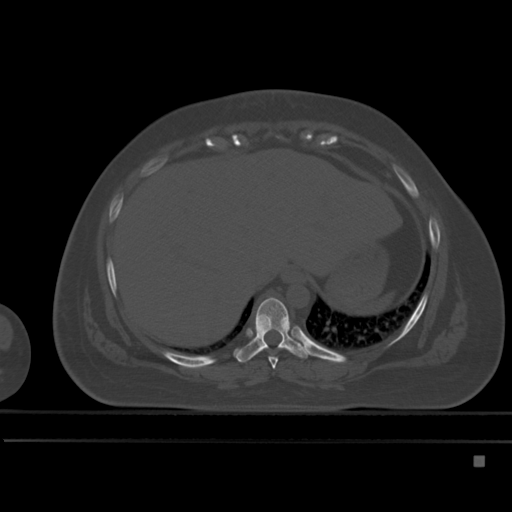
CT including the spine, one axial slice. Position 266 of 495 along the scan axis. Bone window (W 1800 / L 400 HU). 1.5 mm slice thickness. 512 × 512 image matrix, field of view 404 × 404 mm. Female patient, age 33 years. Case-level facts recorded for this patient, not image findings: primary cancer: breast; vertebrae with lytic lesions (as recorded): T1.
Annotated regions visible in this slice (semi-automatically segmented with operator editing):
- T8 vertebra: box from (x=269, y=357) to (x=278, y=369) px
- T9 vertebra: (x=234, y=297)–(x=310, y=363)